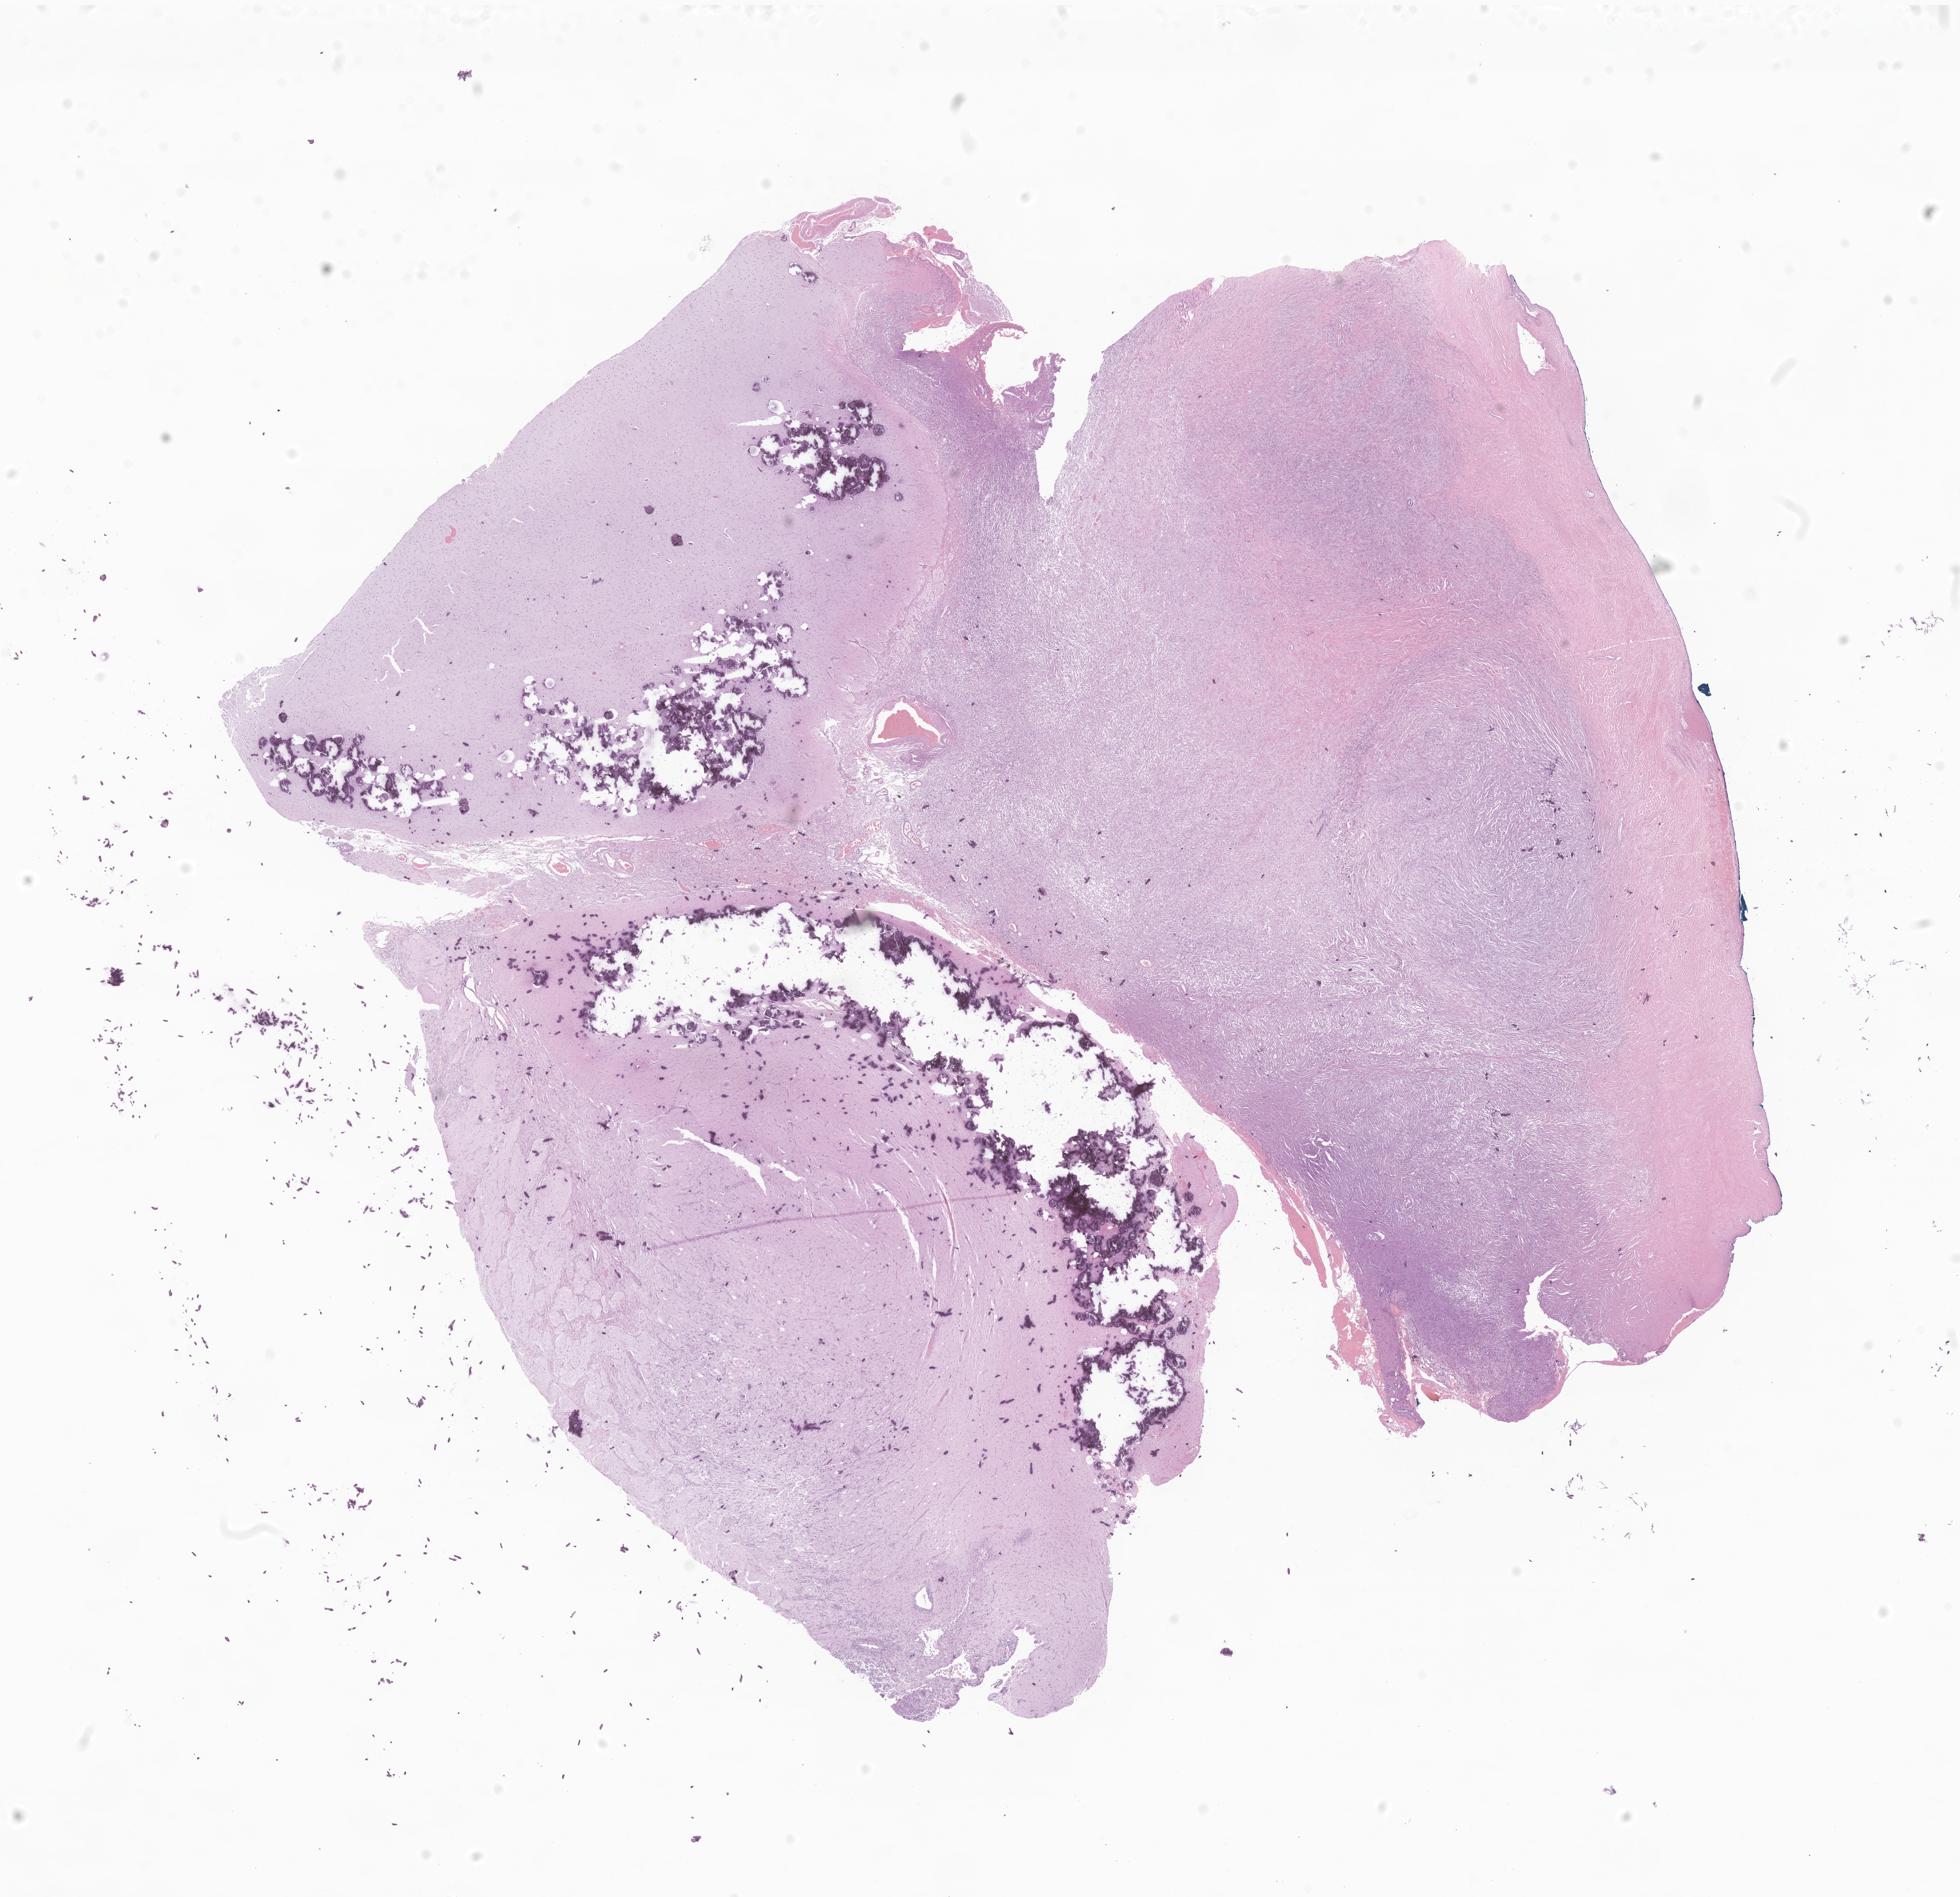
Whole-slide image, H&E stain of tumor tissue from the brain, a low-resolution overview of the entire scanned area, about 20.6 x 19.9 mm. Formalin-fixed, paraffin-embedded (FFPE) tissue. Female patient, age 103 months (8 years 7 months).
Diagnosis (ICD-O-3 morphology term): Neoplasm, uncertain whether benign or malignant.